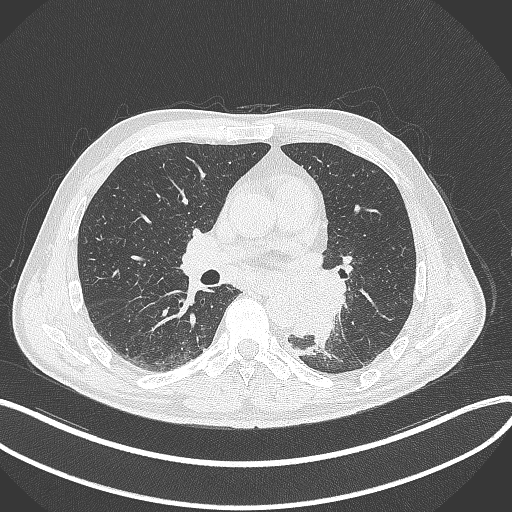
Chest CT, one axial slice. Slice 175 of 329 in the series (ordered by position). Lung window (W 1500 / L -600 HU). 1 mm slice thickness. 512 × 512 image matrix. Male patient, age 59 years. Case-level facts recorded for this patient, not image findings: clinical TNM (as recorded): T2a N2 M0.
Outlined on this slice (rectangle marked by the reading radiologist):
- lung tumour (recorded histology: squamous cell carcinoma): bounding box [x1, y1, x2, y2] px = [265, 264, 344, 346]